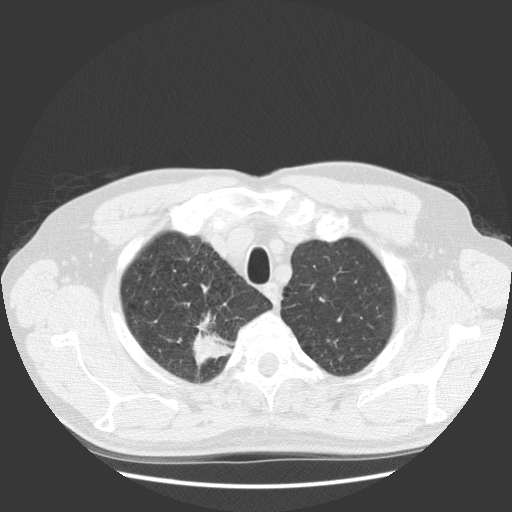
Low-dose screening chest CT, one axial slice; position 110 of 131 along the scan axis; 140 kVp; lung window (W 1500 / L -600 HU); 512 × 512 image matrix, field of view 369 × 369 mm.
Annotated regions visible in this slice (outlined manually by an expert reader):
- lesion 1 (tumor, upper lobe of right lung): box from (x=193, y=314) to (x=235, y=369) px